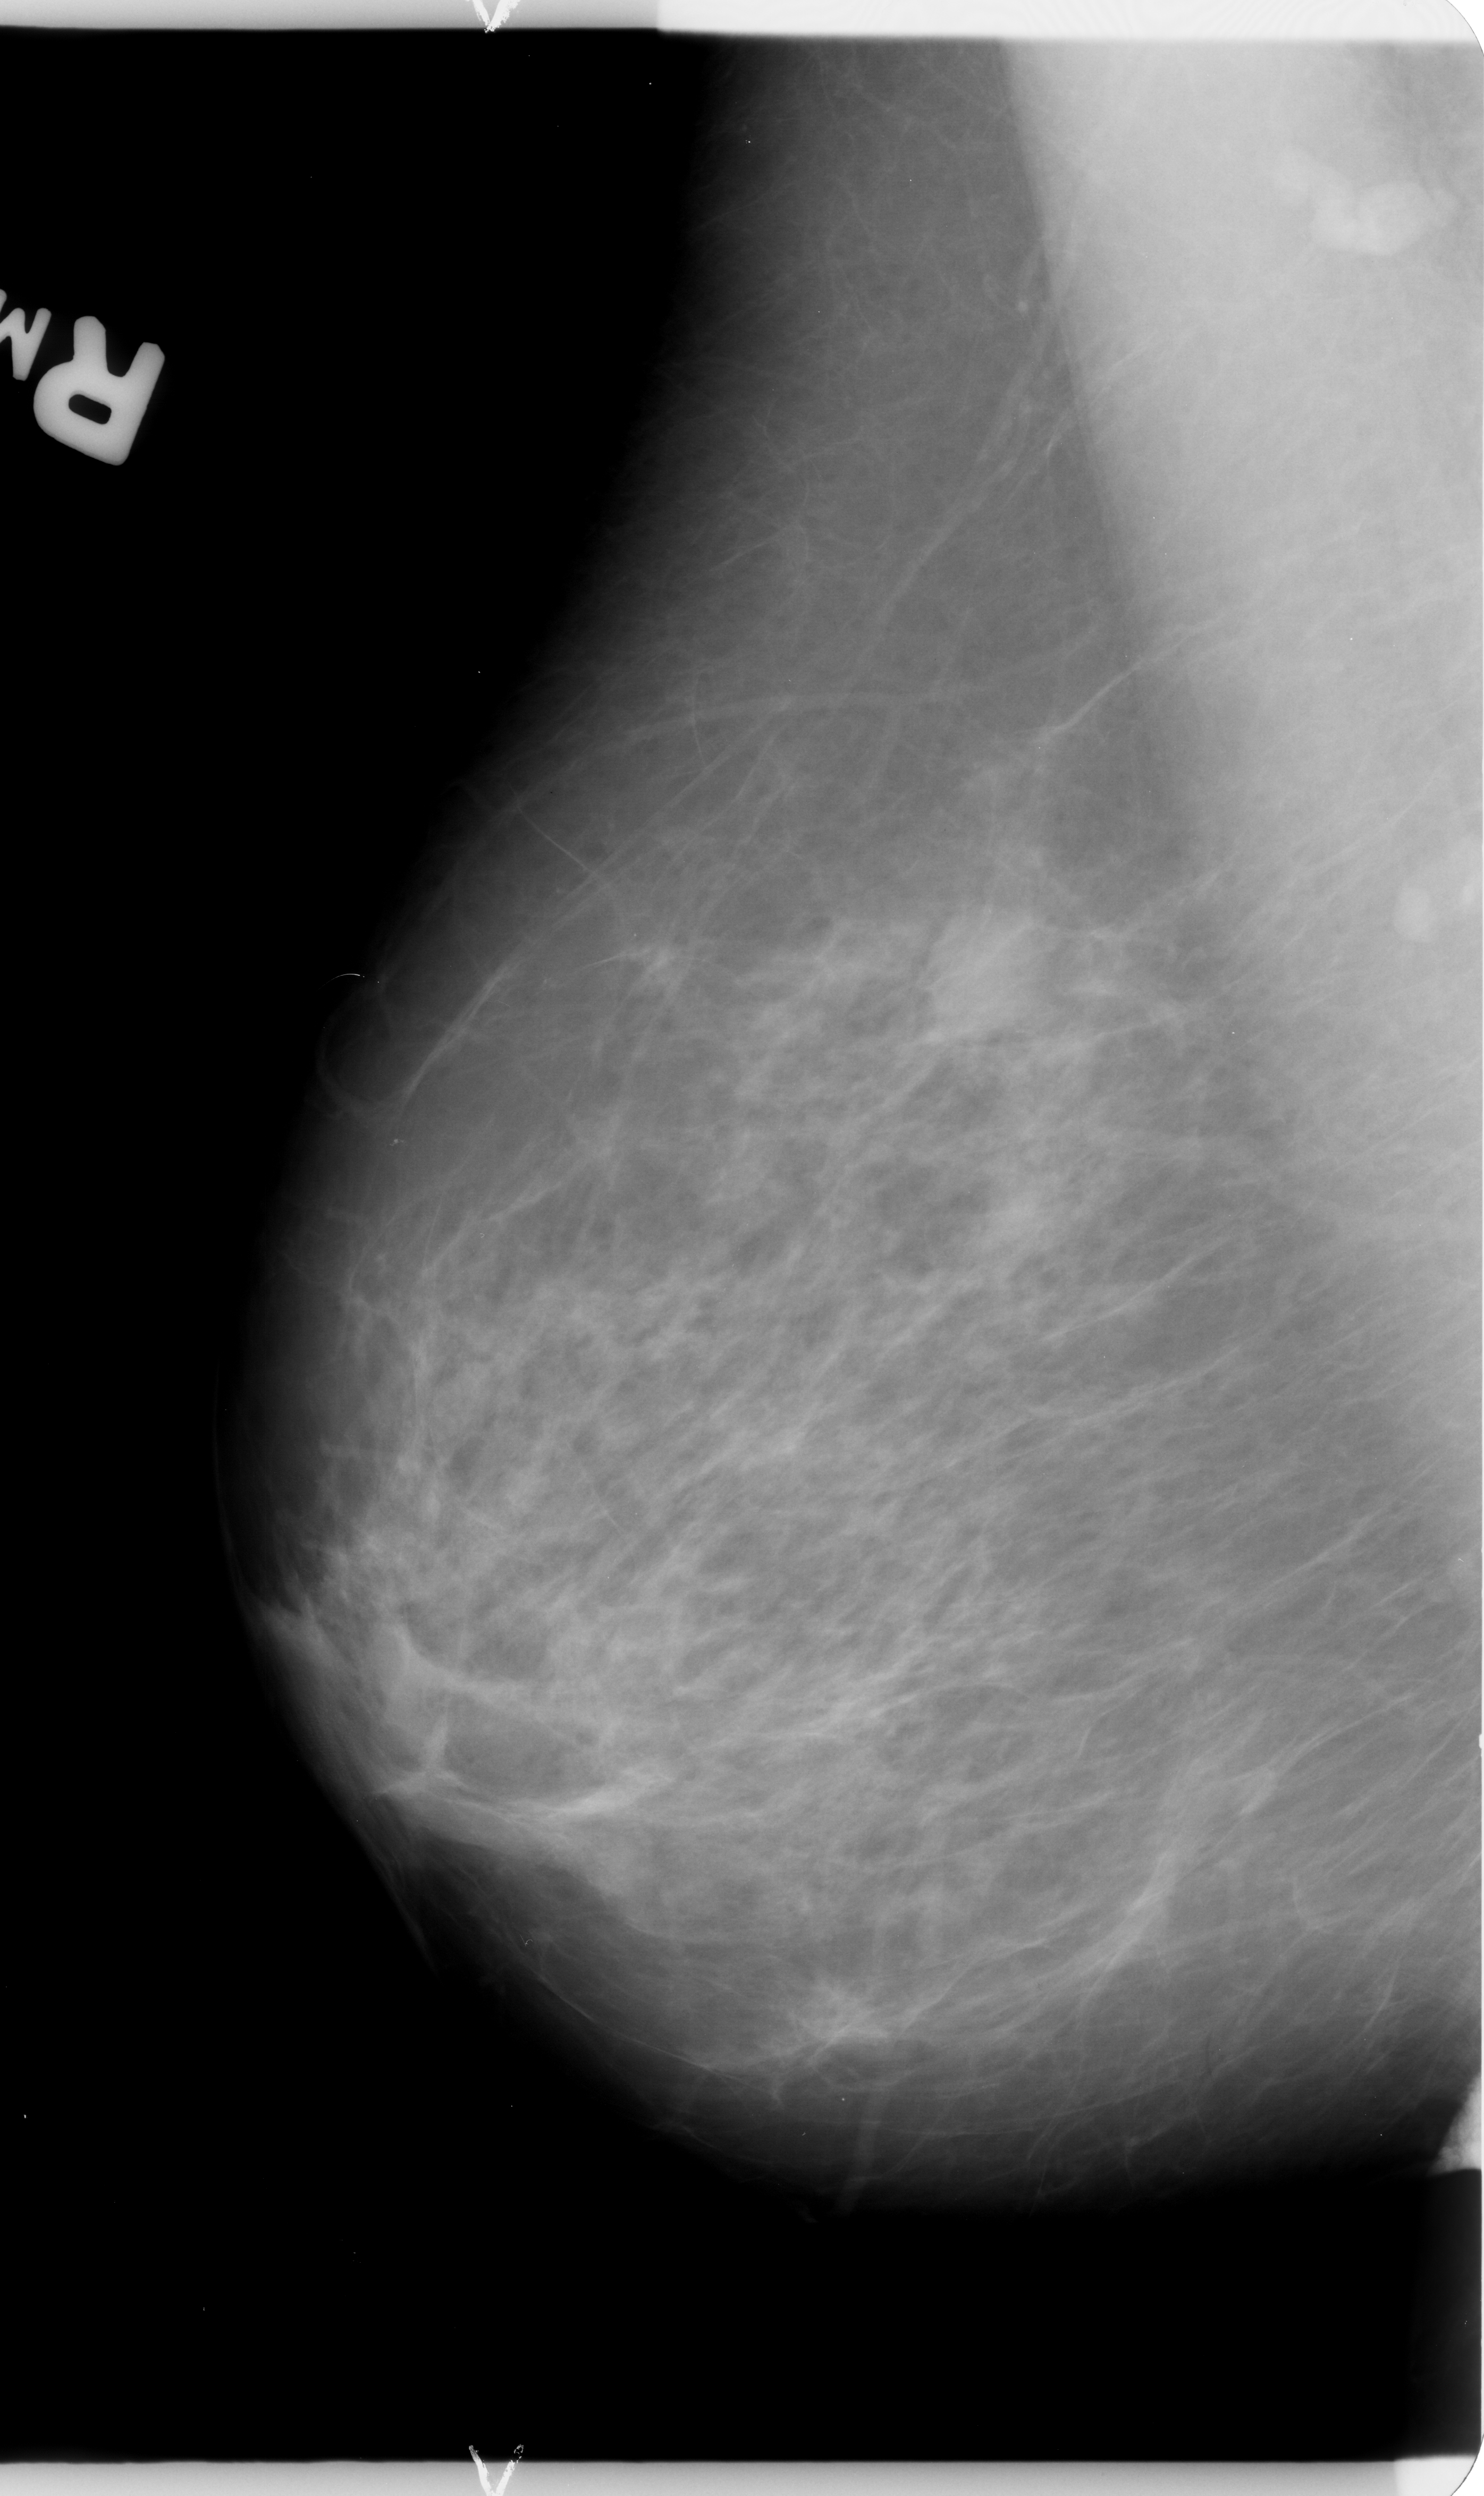
Mammogram (digitized film), right breast, MLO view.
Marked abnormality: mass, shape round, margins circumscribed / ill defined; BI-RADS assessment category 4; subtlety rating 4 on a 1 (subtle) to 5 (obvious) scale; pathology (as recorded): benign.